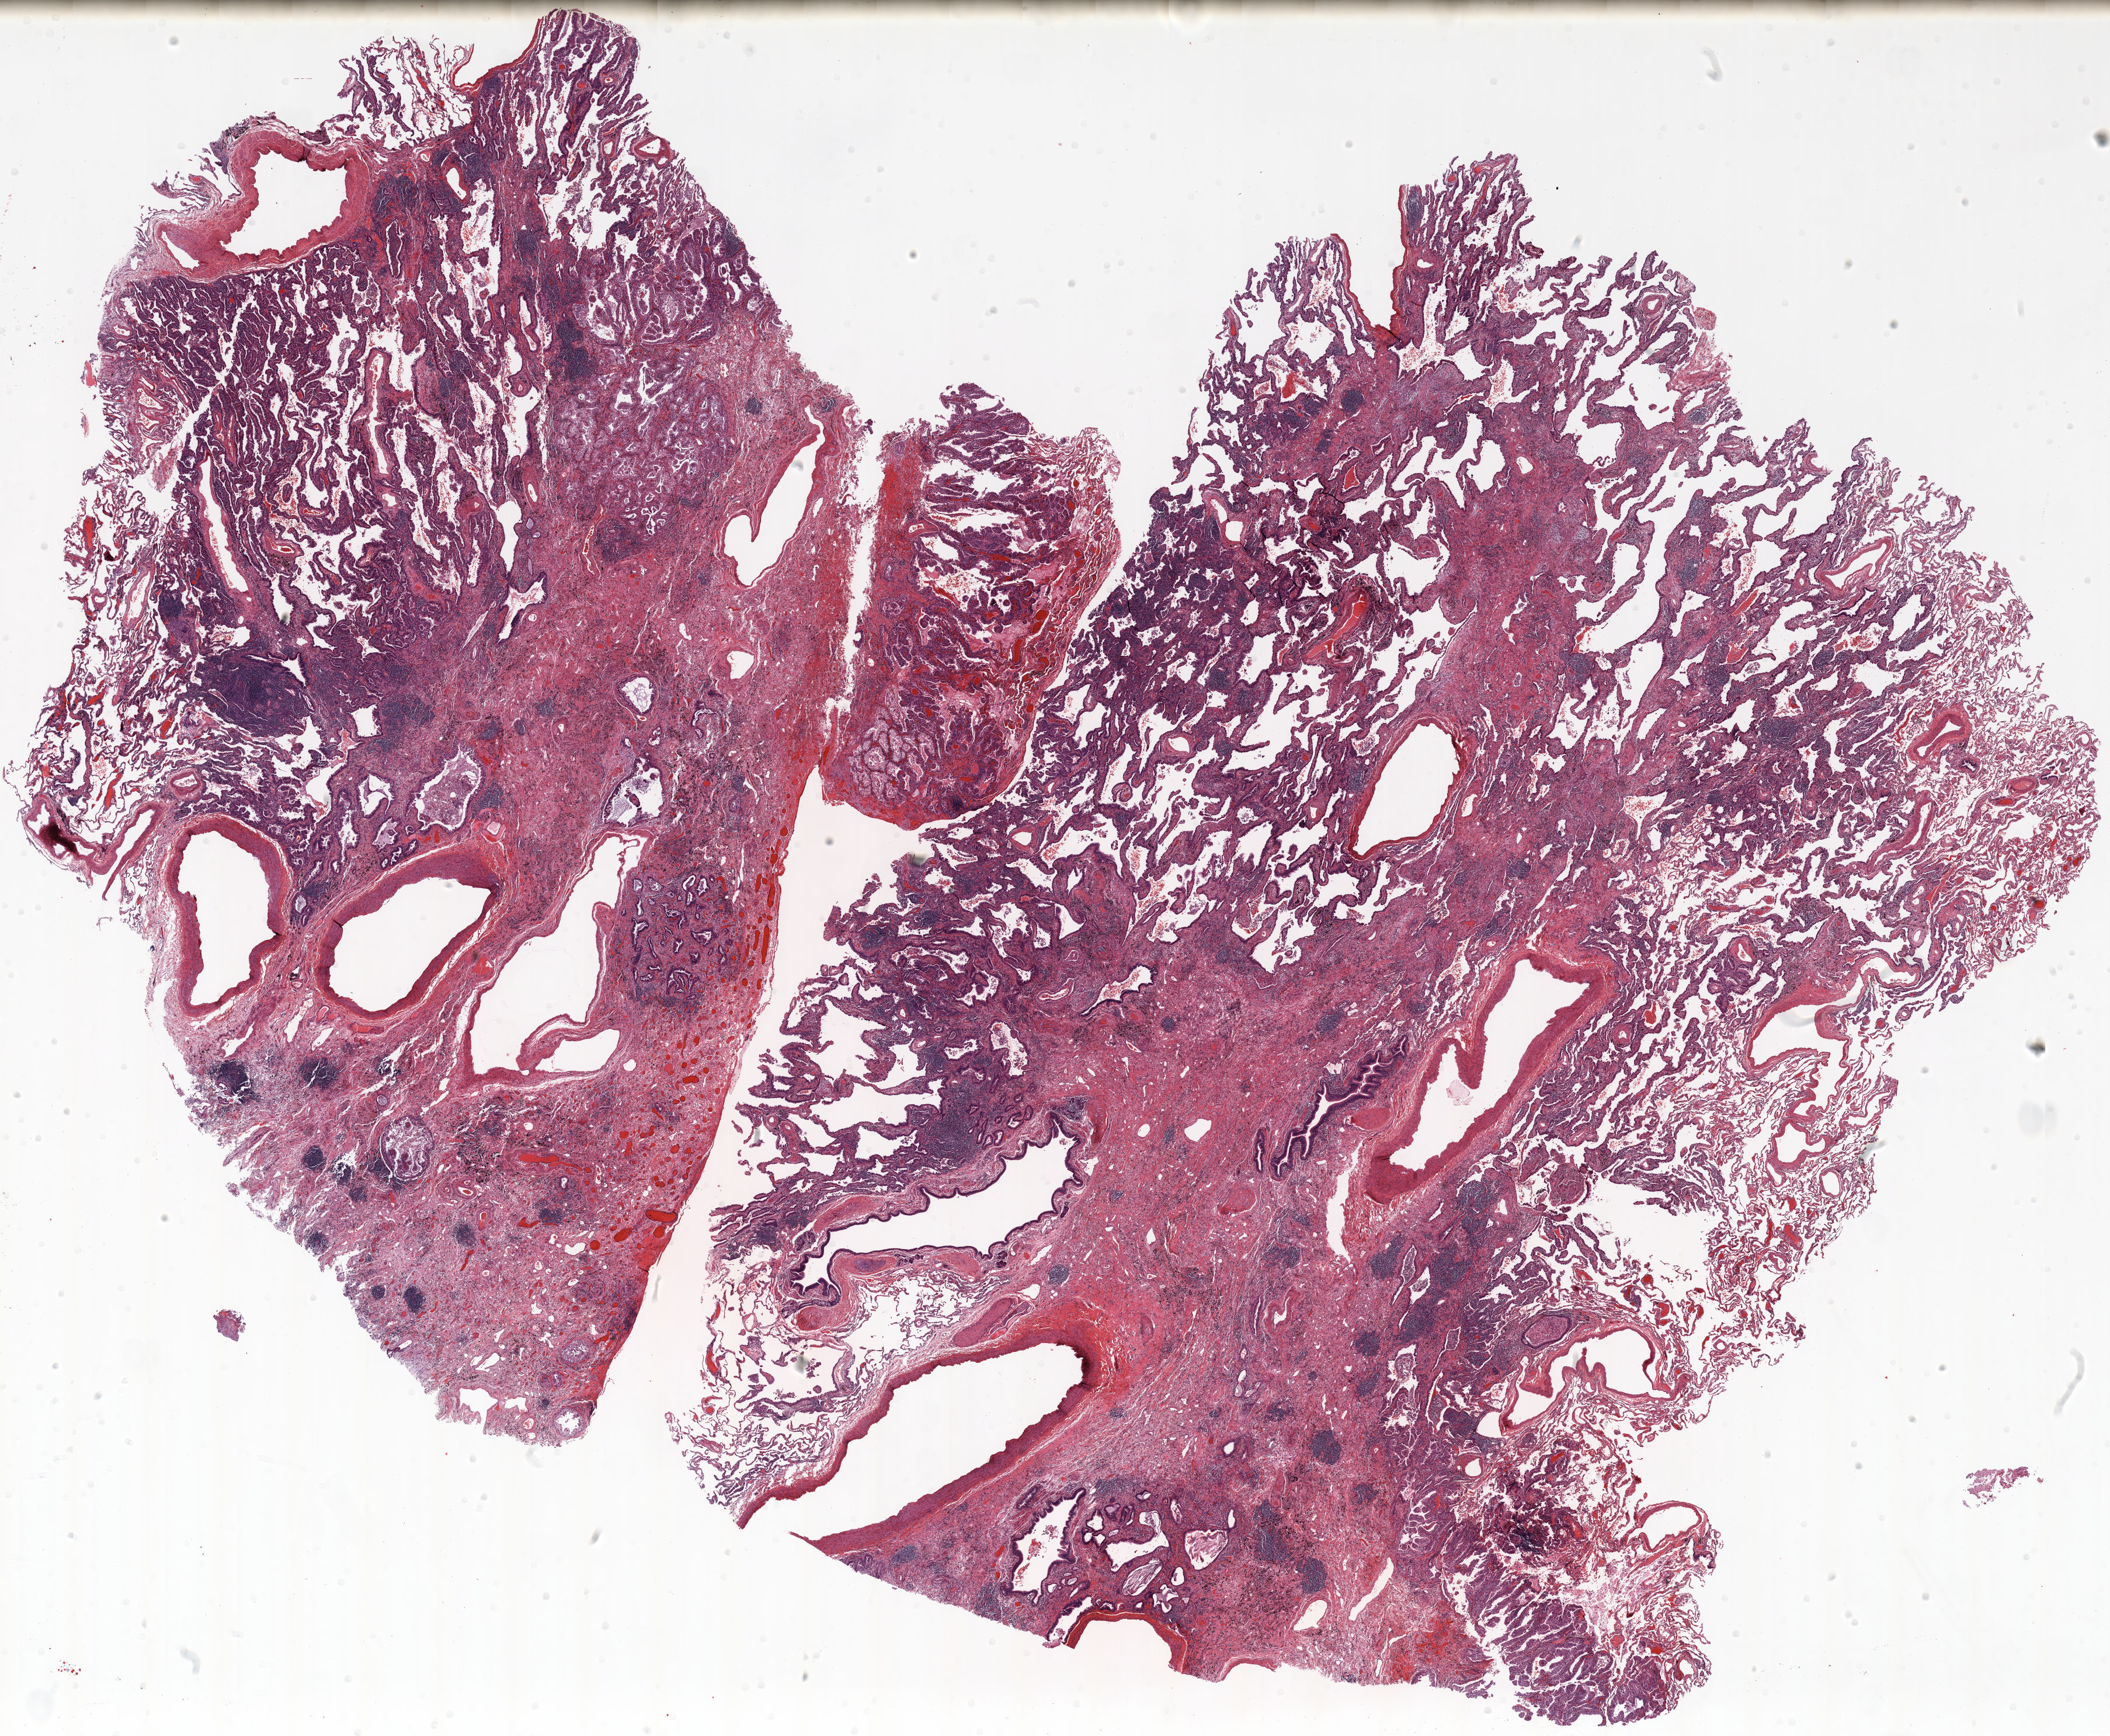
H&E whole-slide image, a low-resolution overview of the entire scanned area, about 29.0 x 23.9 mm, FFPE section, lung. Female patient, aged 57 at enrolment. Former smoker at enrolment. Grade: moderately differentiated (G2).
Participant's lung-cancer diagnosis: Adenocarcinoma with mixed subtypes. Tumour size (pathology): 19 mm. Stage (AJCC 6th edition): IIIB. Primary tumour location (clinical record): left upper lobe.